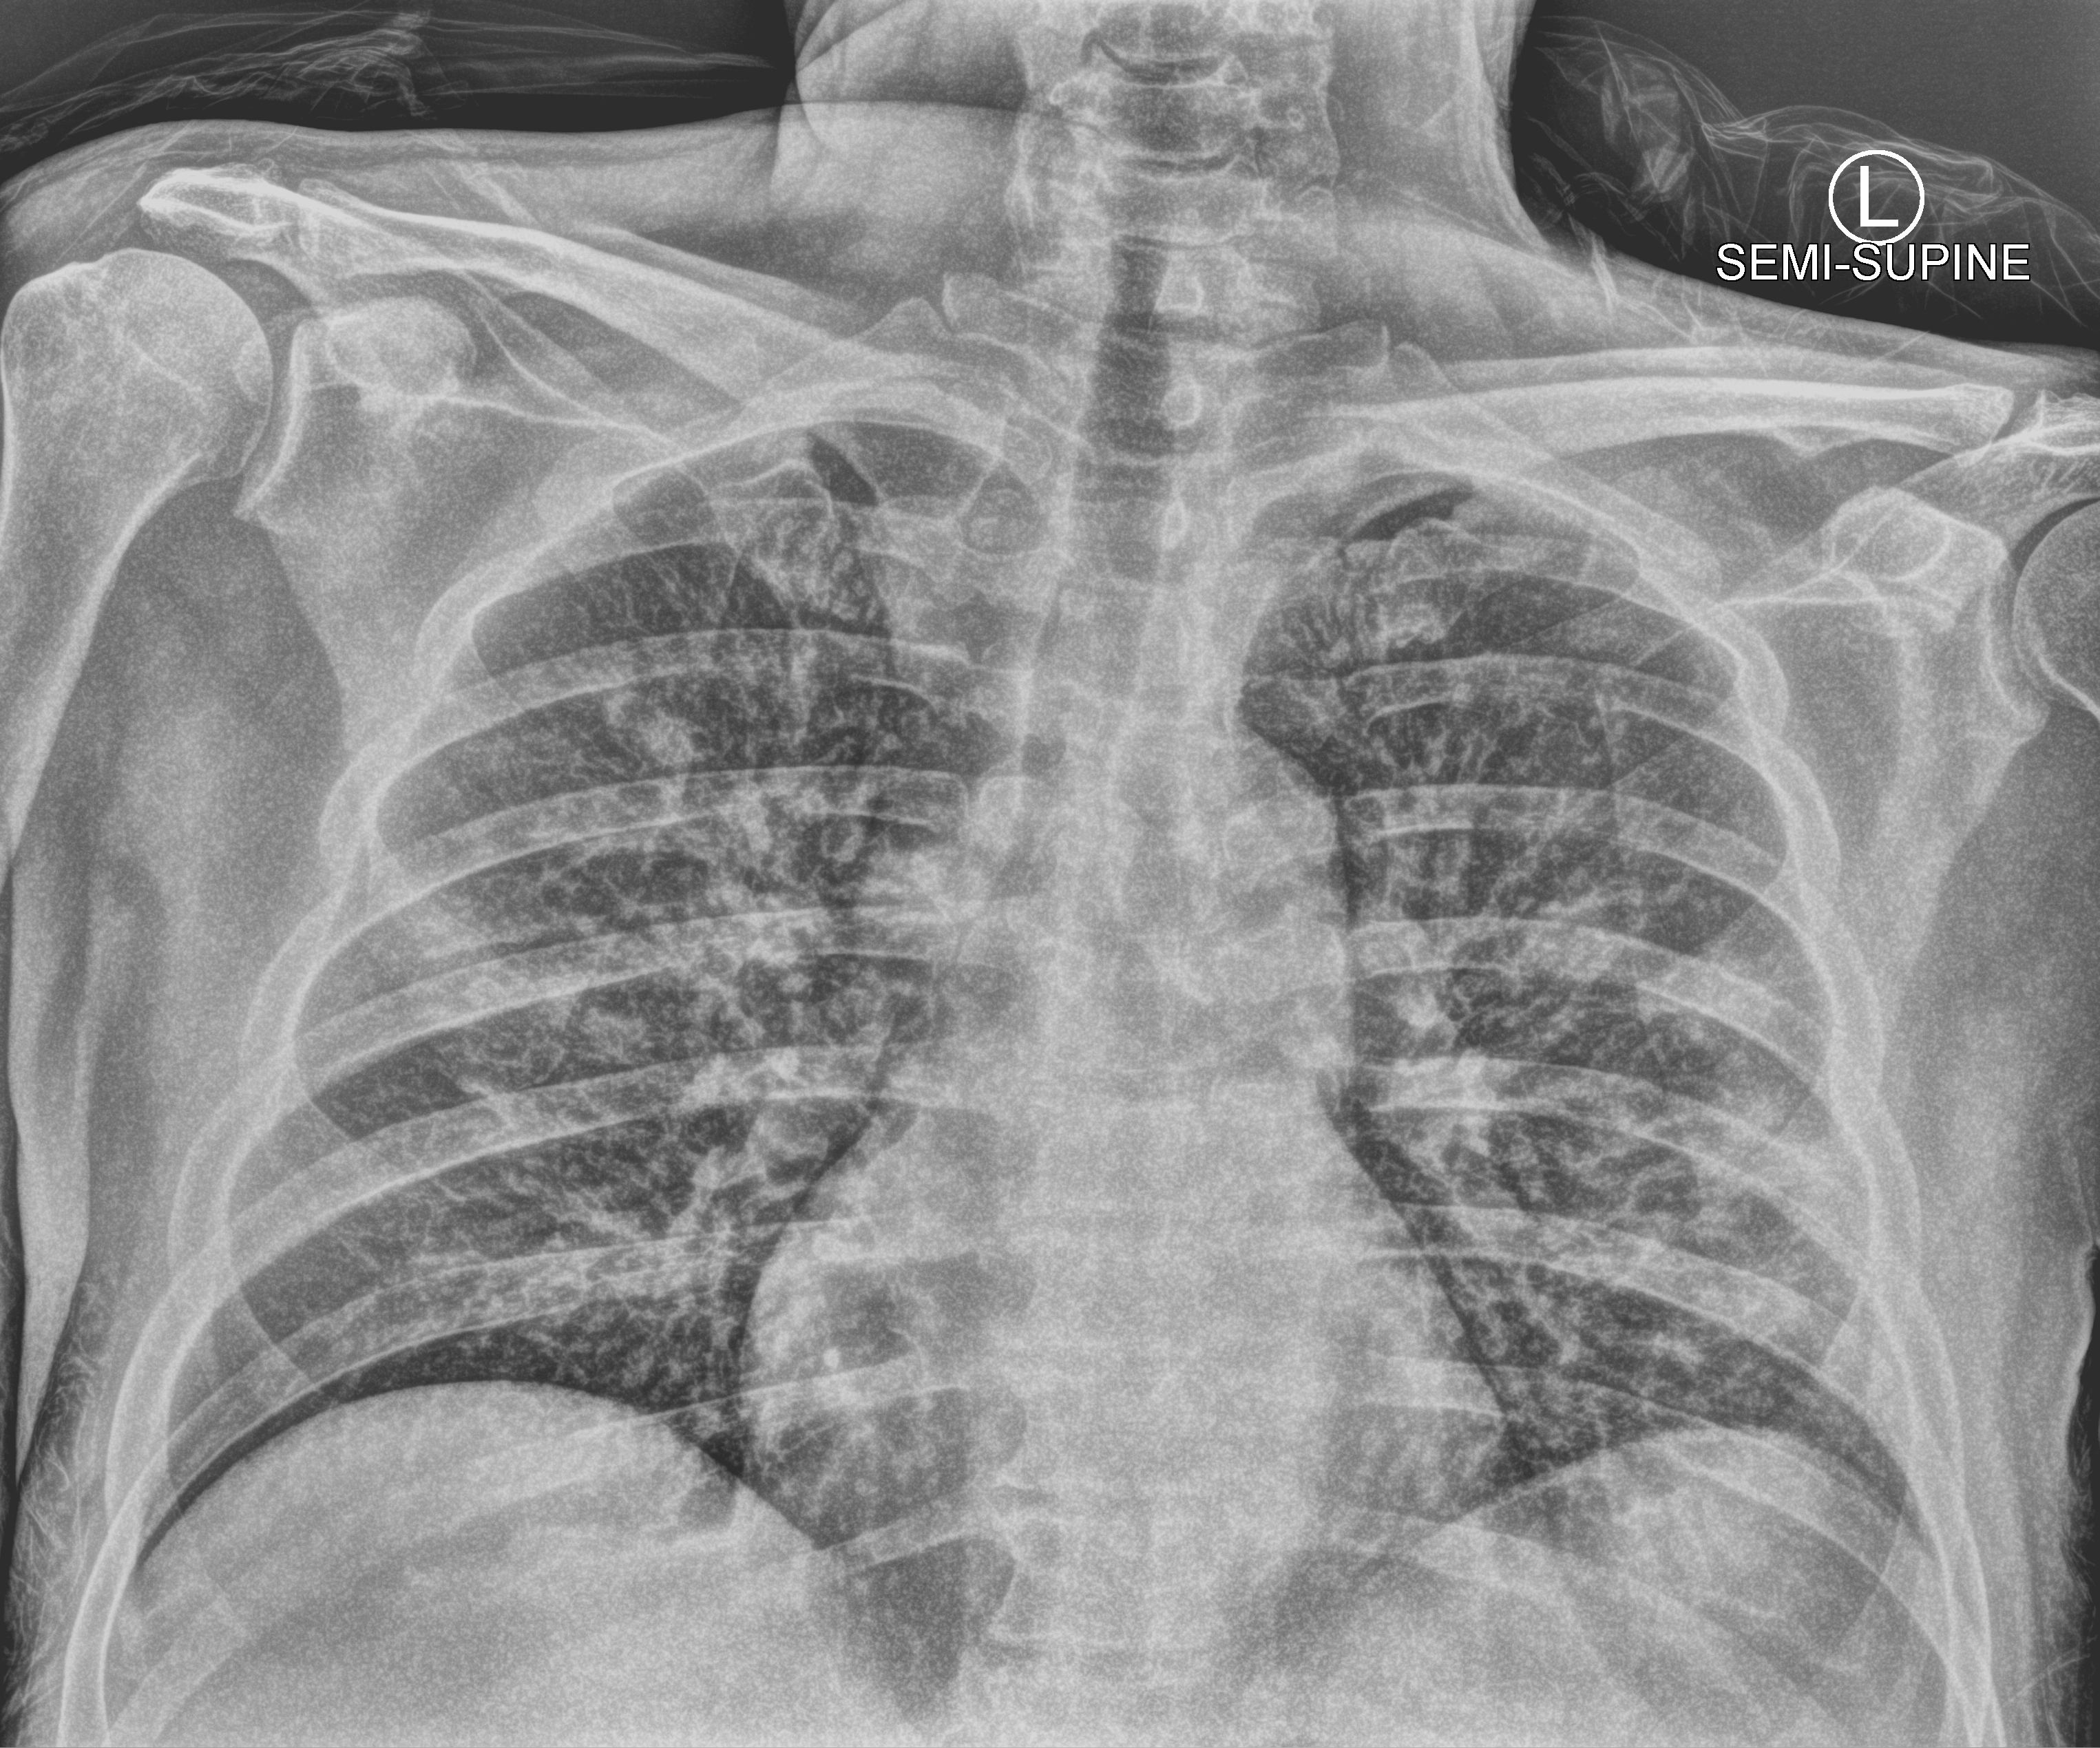
Bedside chest radiograph (computed radiography). Patient hospitalised with COVID-19; male, aged 18–59 years.
Admission-level facts for this patient (not findings on this image; timing relative to this image not recorded):
- admitted to intensive care during this hospital stay: no
- chronic kidney disease (admission record): no